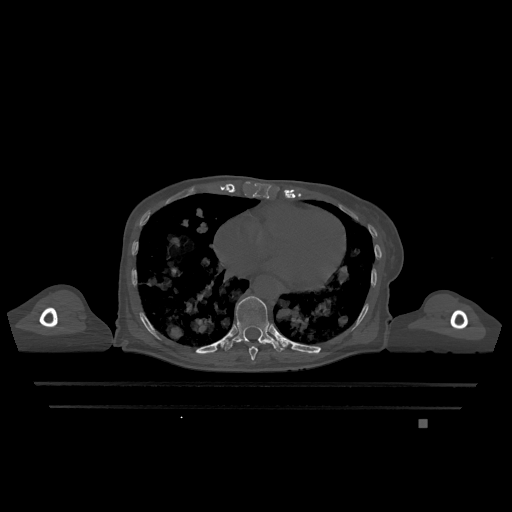
CT including the spine, one axial slice; slice 660 of 1317 in the series (ordered by position); bone window (W 1800 / L 400 HU); 0.5 mm slice thickness; 512 × 512 image matrix, field of view 500 × 500 mm. Female patient, age 74 years. From the clinical record (not read from this slice): primary cancer: lung.
Structures marked on this image (semi-automatic segmentation, software-assisted and operator-edited):
- T10 vertebra: bounding box [x1, y1, x2, y2] px = [223, 296, 283, 353]
- T9 vertebra: [249, 340, 259, 361]